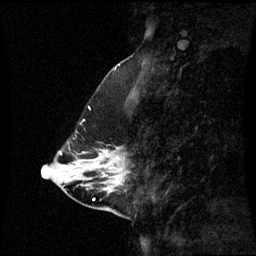
Breast MRI (dynamic contrast-enhanced), one sagittal slice; dynamic contrast-enhanced series, image 2 of 3 at this slice position (ordered by acquisition); 1.5 T; TE 4.2 ms, TR 8.9 ms; 256 × 256 image matrix, field of view 240 × 240 mm. Female patient, age 43 years. Case-level facts recorded for this patient, not image findings: setting: breast cancer imaged before/during neoadjuvant chemotherapy; receptor status: HR-positive, HER2-negative.
Outlined on this slice (semi-automatic segmentation, software-assisted and operator-edited):
- analysis volume of interest (the breast-tissue region the enhancement analysis was run in; not a lesion): bounding box <78,148,129,193> (left, top, right, bottom; pixels)
- tumour enhancement mask (voxels above the 70 % enhancement threshold inside the analysis volume of interest): <98,166,103,167>